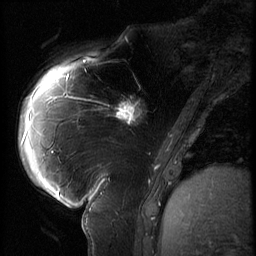
Breast MRI (dynamic contrast-enhanced), one sagittal slice; position 21 of 62 along the scan axis; 3 images stored at this slice position (order not interpretable as contrast timing); 1.5 T; TE 4.2 ms, TR 9 ms; 2.5 mm slice thickness; 256 × 256 image matrix, field of view 180 × 180 mm. Patient: female, 57 years. From the clinical record (not read from this slice): setting: breast cancer imaged before/during neoadjuvant chemotherapy; receptor status: triple-negative.
Annotated regions visible in this slice (semi-automatic segmentation, software-assisted and operator-edited):
- analysis volume of interest (the breast-tissue region the enhancement analysis was run in; not a lesion): bounding box (x1, y1, x2, y2) in pixels: (105, 84, 158, 135)
- tumour enhancement mask (voxels above the 140 % enhancement threshold inside the analysis volume of interest): (114, 96, 142, 125)